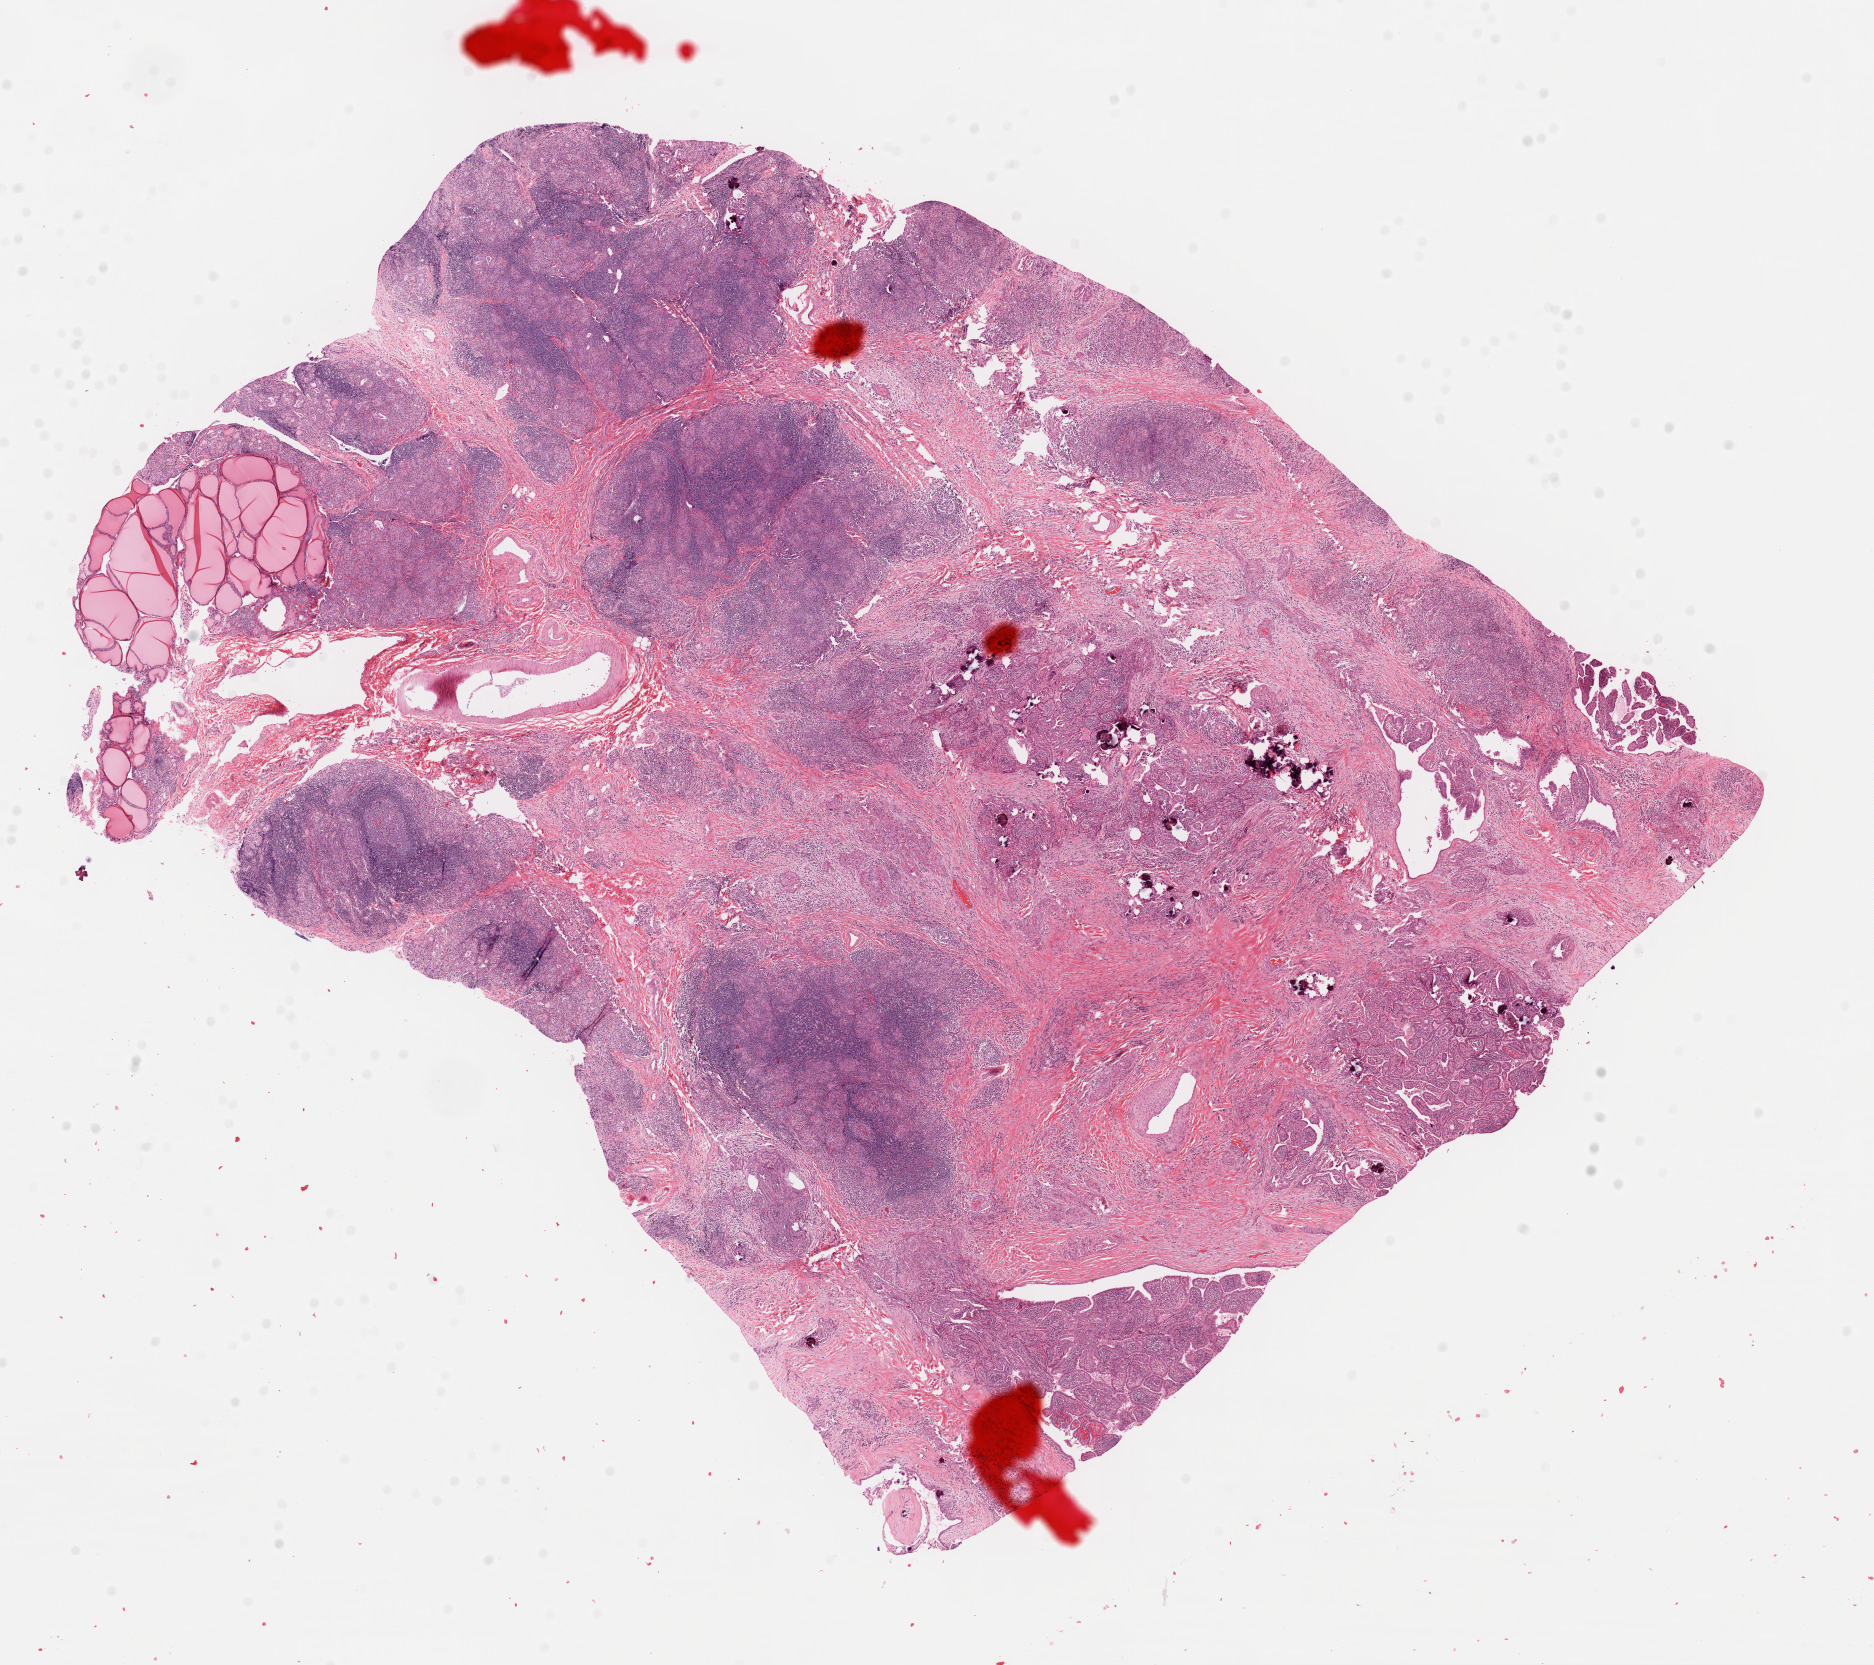
Digitized Hematoxylin and eosin (H&E) stained tissue section (whole slide) — a low-resolution overview of the entire scanned area, about 14.8 x 13.2 mm. Formalin-fixed paraffin-embedded (FFPE) diagnostic section. Primary tumour sample from the thyroid. Female, age 18 years at initial diagnosis.
AJCC pathologic stage: I. Diagnosis: Papillary adenocarcinoma, NOS. TNM: T3 N1a M0. Lymph nodes positive (case pathology): 11 of 14 examined.